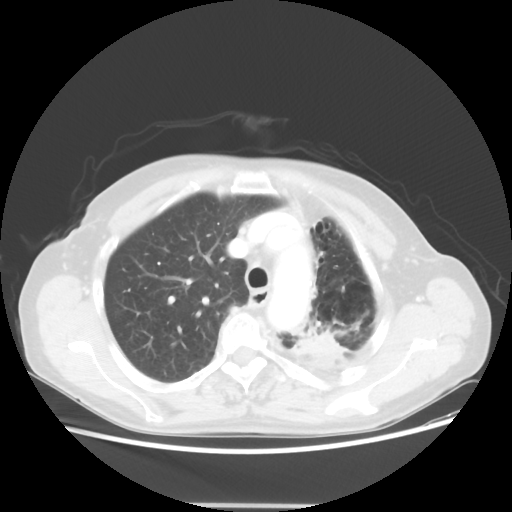
Chest CT, one axial slice; slice 40 of 56 in the series (ordered by position); reconstruction kernel STANDARD; lung window (W 1500 / L -600 HU); 512 × 512 image matrix. Patient: female, 63 years. From the clinical record (not read from this slice): clinical TNM (as recorded): T2a N0 M0.
Outlined on this slice (bounding box drawn by a radiologist):
- lung tumour (recorded histology: adenocarcinoma): bounding box (x1, y1, x2, y2) in pixels: (297, 326, 348, 363)